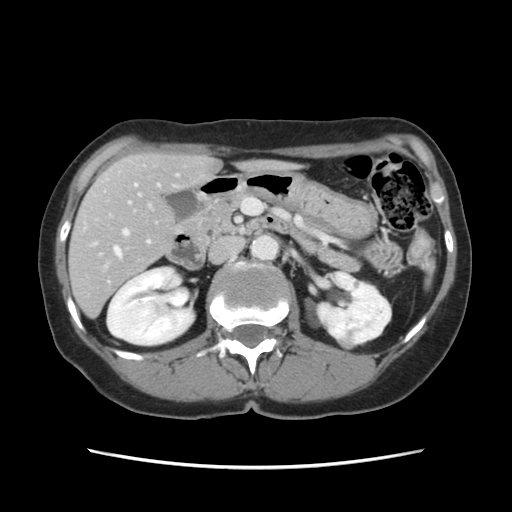
Contrast-enhanced abdominal CT, one axial slice; slice 57 of 120 in the series (ordered by position); 120 kVp; intravenous contrast given; soft-tissue window (W 400 / L 40 HU); 2.5 mm slice thickness; 512 × 512 image matrix, field of view 330 × 330 mm. Female patient, age 70 years. From the clinical record (not read from this slice): diagnosis: colorectal cancer liver metastases, imaged before liver resection; multiple liver metastases: no.
Outlined on this slice (manually delineated by an expert):
- hepatic veins: box from (x=114, y=247) to (x=121, y=257) px
- liver: (x=70, y=153)–(x=270, y=315)
- planned liver remnant (the part of the liver to remain after resection): (x=71, y=153)–(x=276, y=302)
- portal vein (with intrahepatic branches): (x=94, y=175)–(x=178, y=245)